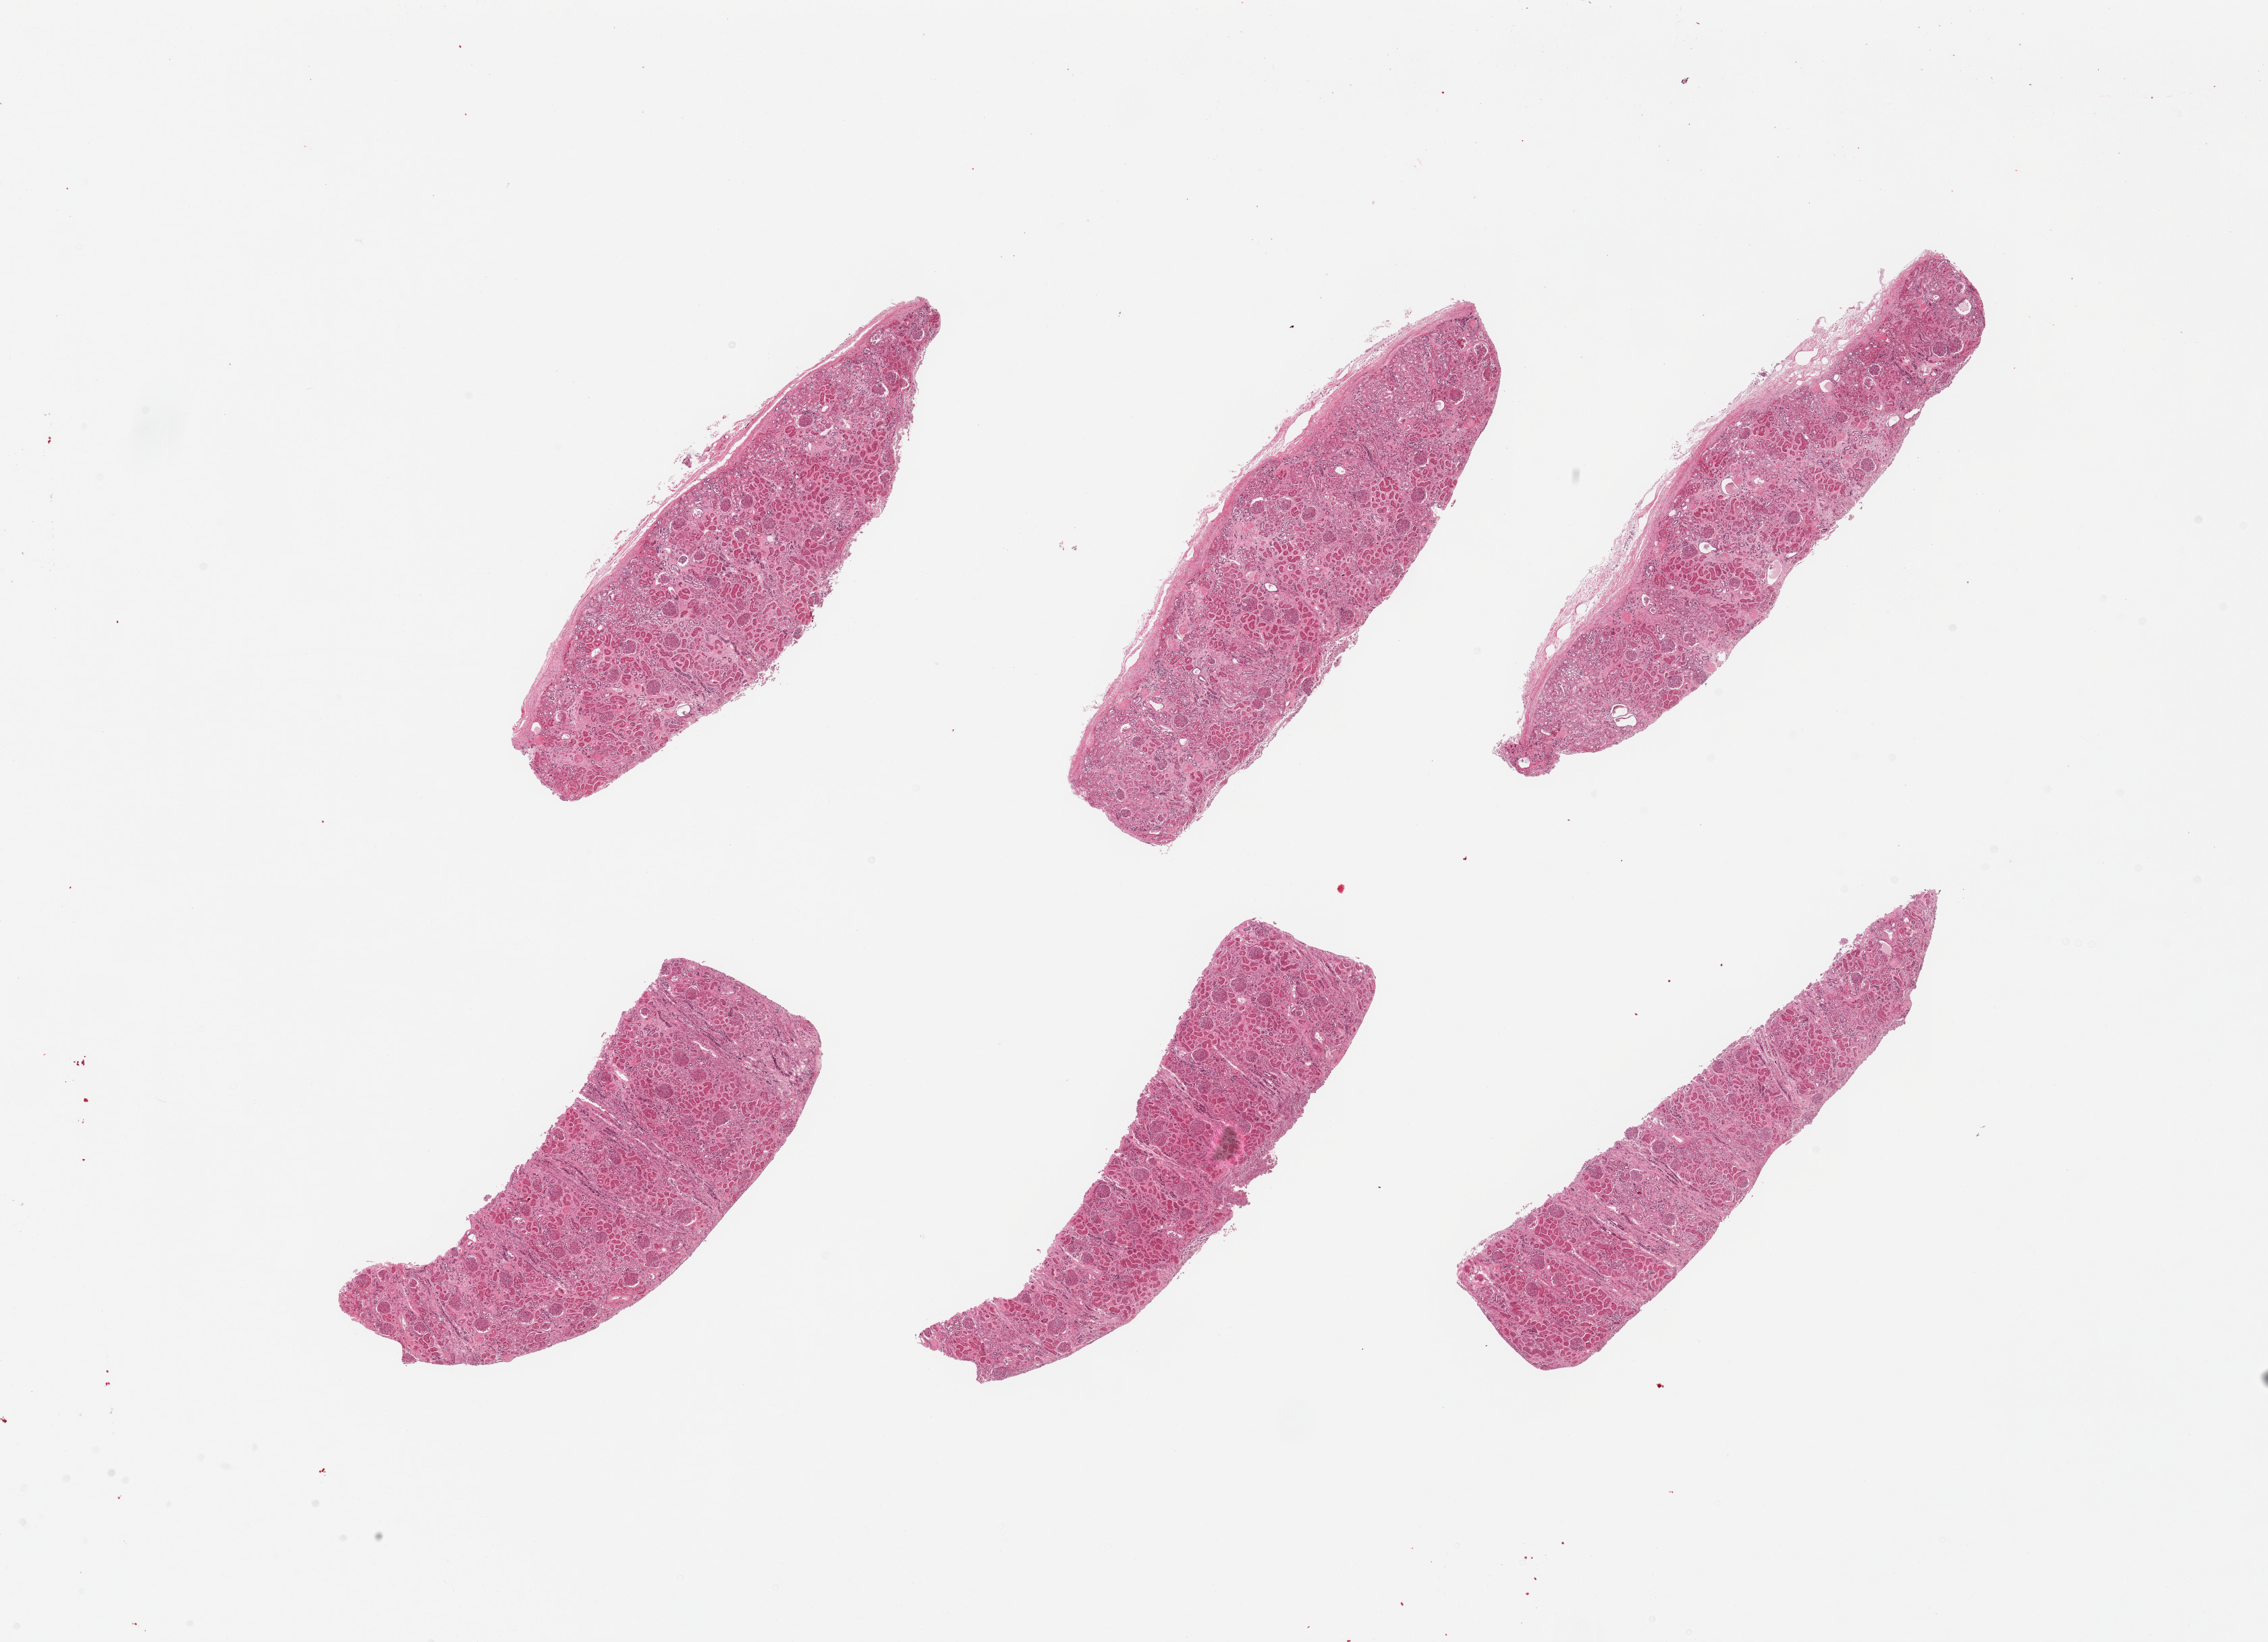
Whole-slide image, H&E stain, brightfield — a low-resolution overview of the entire scanned area, about 26.6 x 19.2 mm, PAXgene-fixed, paraffin-embedded tissue, sampled site (target tissue): renal cortex, donor tissue sample. Male donor.
- pathologist's review note for this sample: 6 pieces; scattered sclerosed glomeruli; severe tubular autolysis